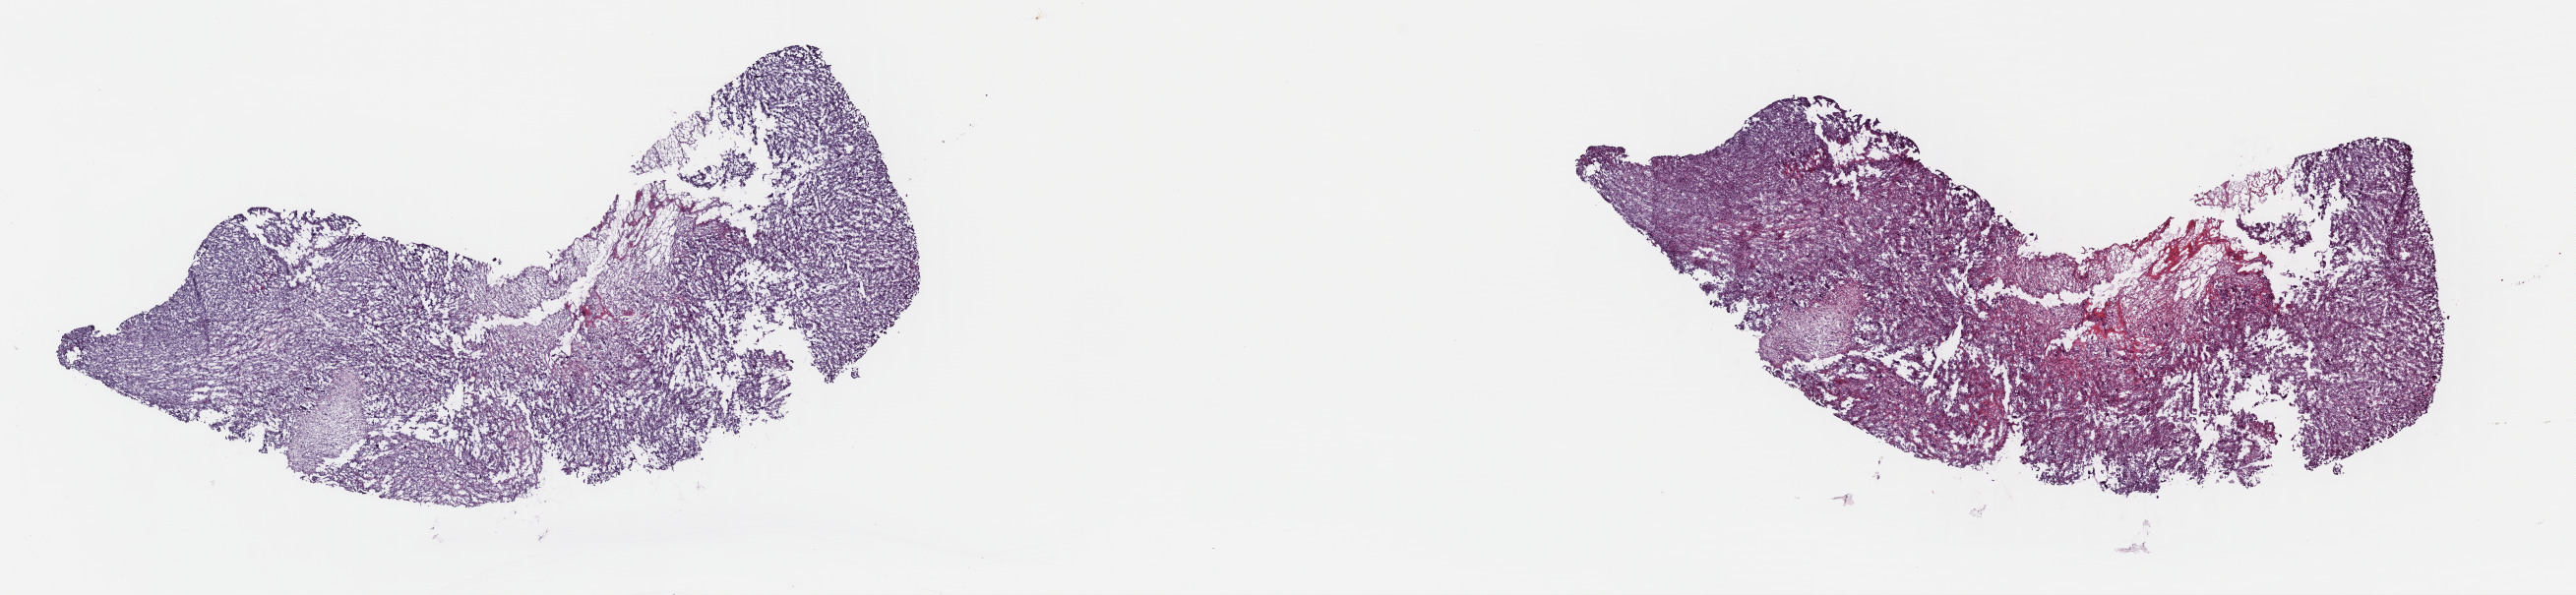
H&E-stained whole-slide image, whole scanned area (about 20.6 x 4.8 mm, acquisition: 40x scan) shown as a low-resolution overview, frozen section from the top of the tissue portion, connective, subcutaneous and other soft tissues, primary tumour sample. Patient: male, age at initial diagnosis 42 years. Composition of this section per pathologist review: tumour cells 80%, tumour nuclei 80%, normal cells 0%, stromal cells 20%, necrosis 0%. Inflammatory infiltration, as recorded: lymphocyte infiltration 0%, monocyte infiltration 0%, neutrophil infiltration 0%.
Diagnosis: Malignant fibrous histiocytoma (connective, subcutaneous and other soft tissues of pelvis).